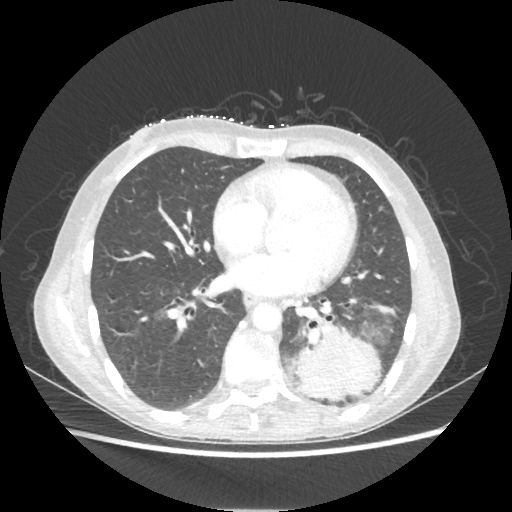
Chest CT, one axial slice. Slice 94 of 221 in the series (ordered by position). 80 kVp. Lung window (W 1500 / L -600 HU). 1.25 mm slice thickness. 512 × 512 image matrix, field of view 360 × 360 mm. Patient: female, 53 years. Case-level facts recorded for this patient, not image findings: clinical TNM (as recorded): T3 N0 M0.
Annotated regions visible in this slice (bounding box drawn by a radiologist):
- lung tumour (recorded histology: adenocarcinoma): bounding box <291,322,380,399> (left, top, right, bottom; pixels)